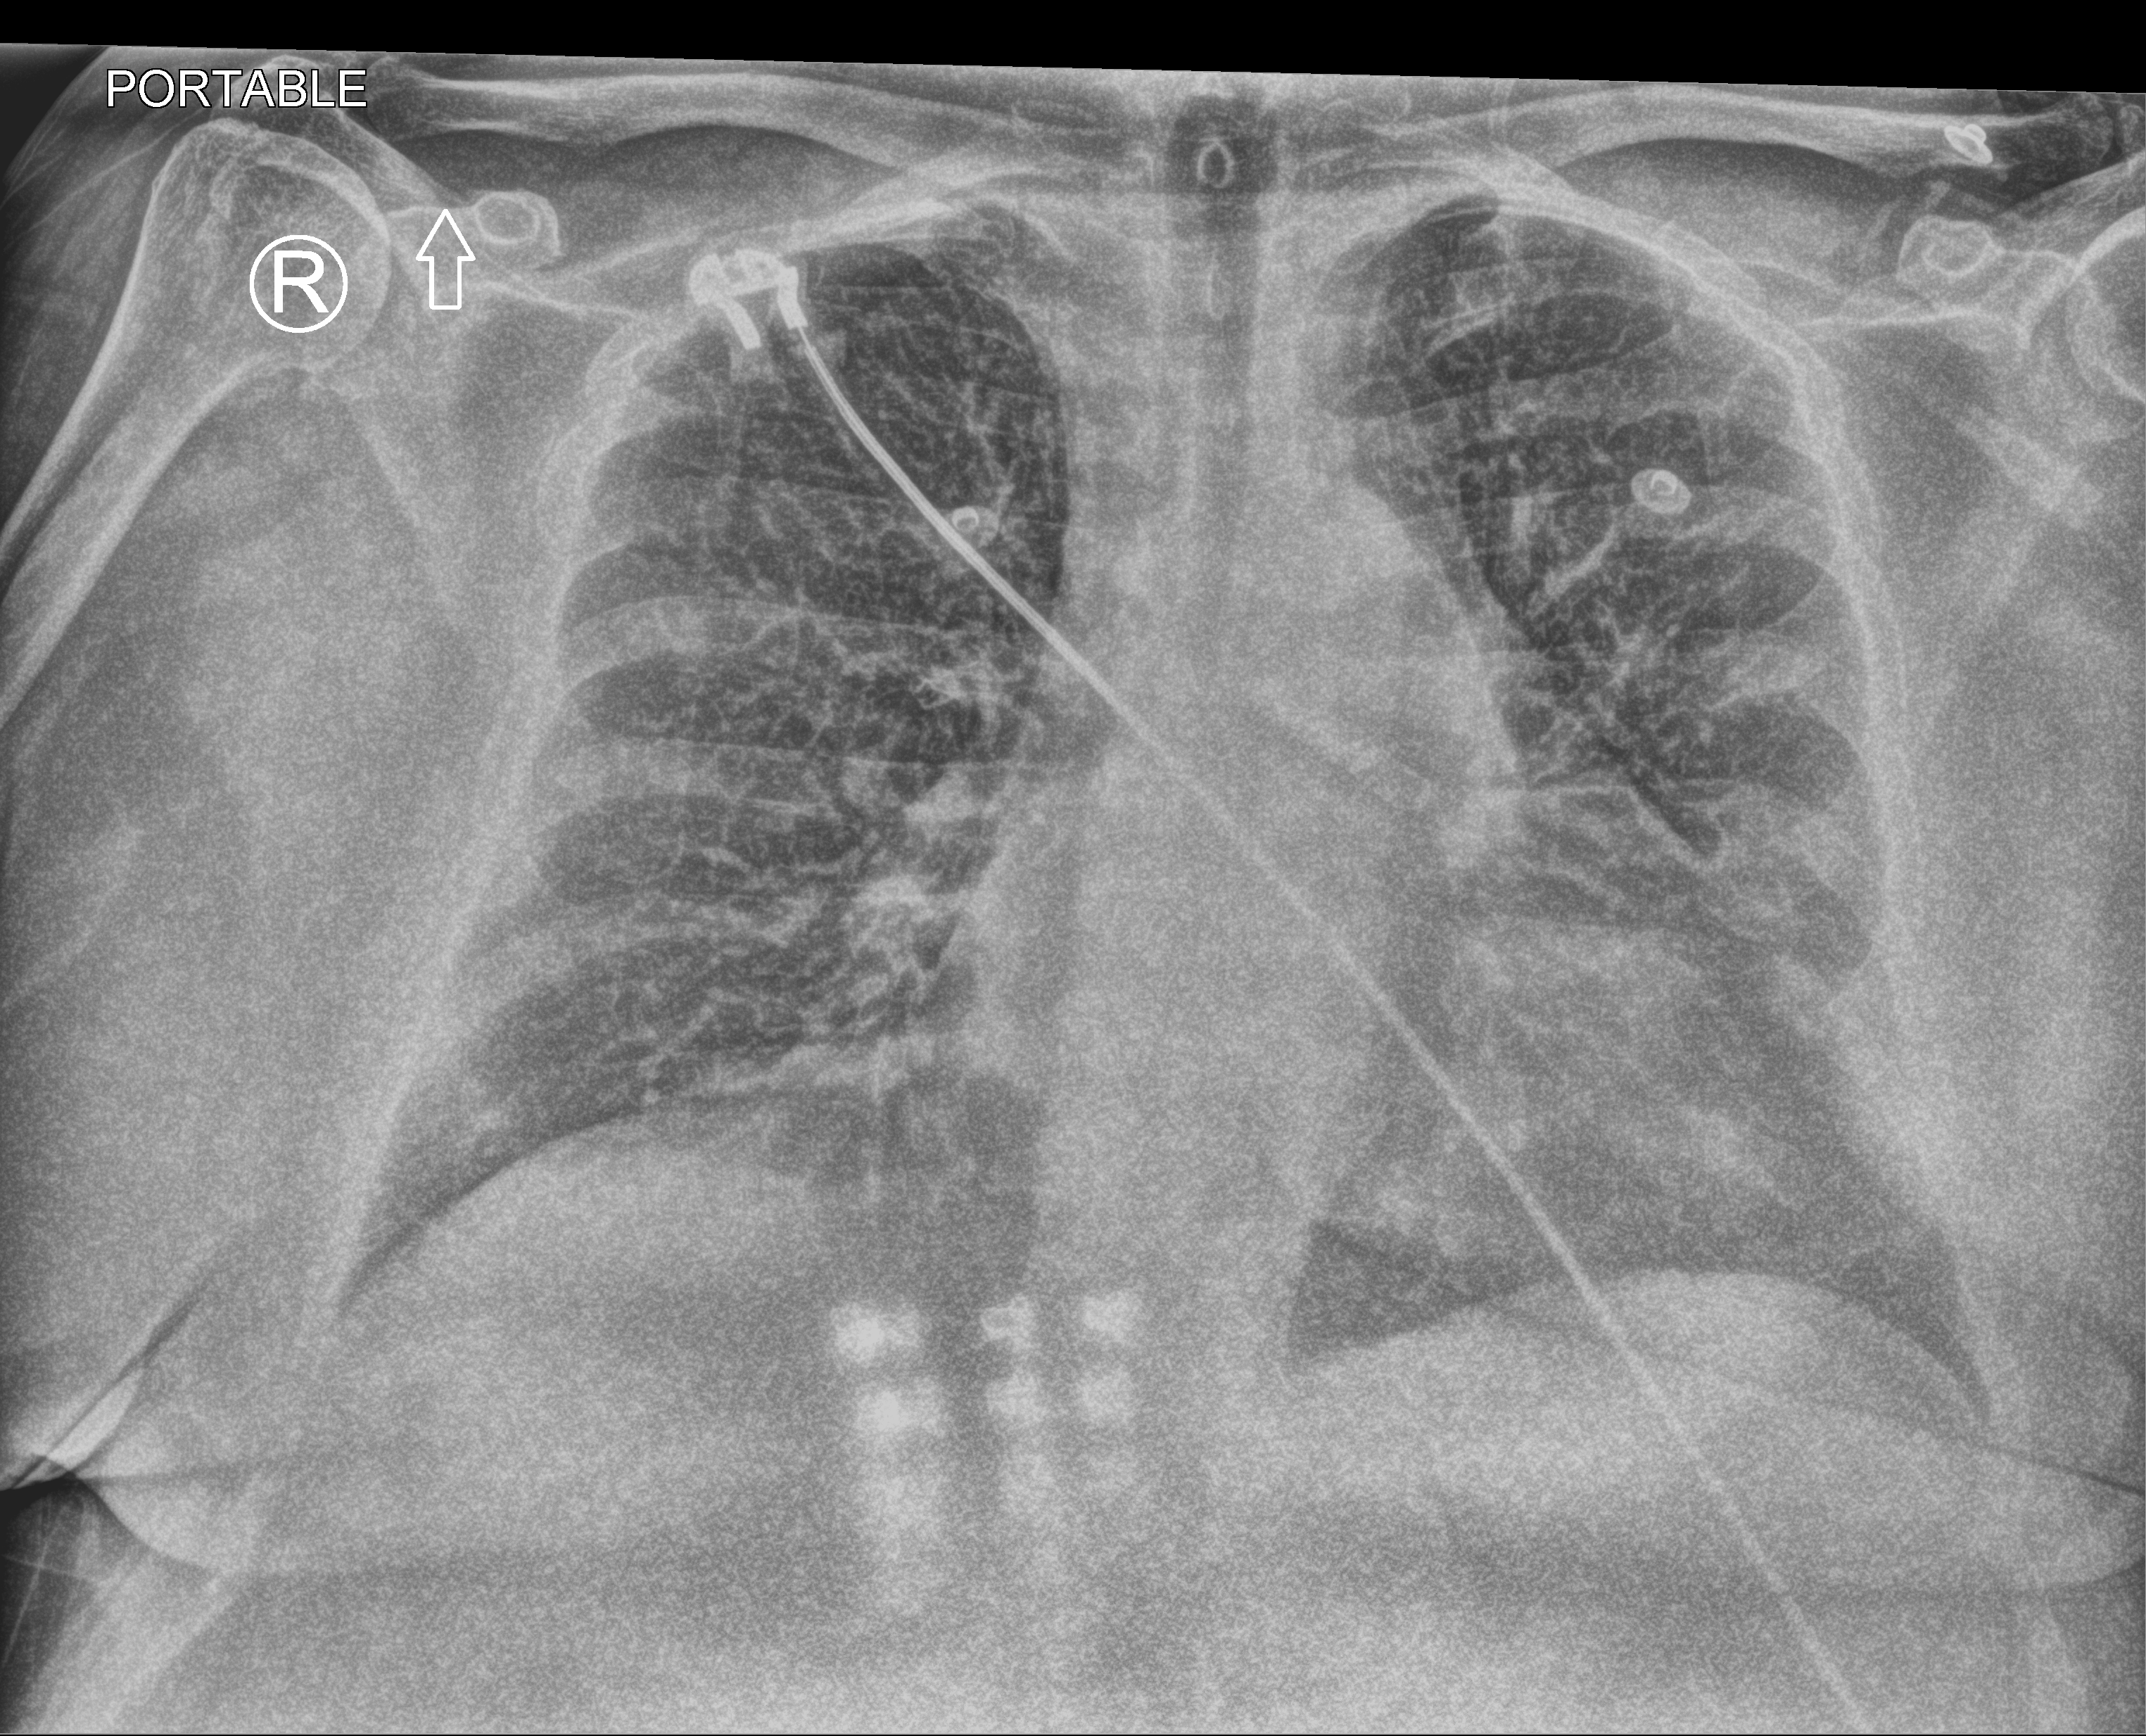
Portable chest radiograph, anteroposterior (AP) projection. Female patient hospitalised with COVID-19, age 60–74 years.
Hospital-stay facts (about this admission, not read from this image; timing relative to this image not recorded): length of hospital stay: 28 days; admitted to intensive care during this hospital stay: yes.